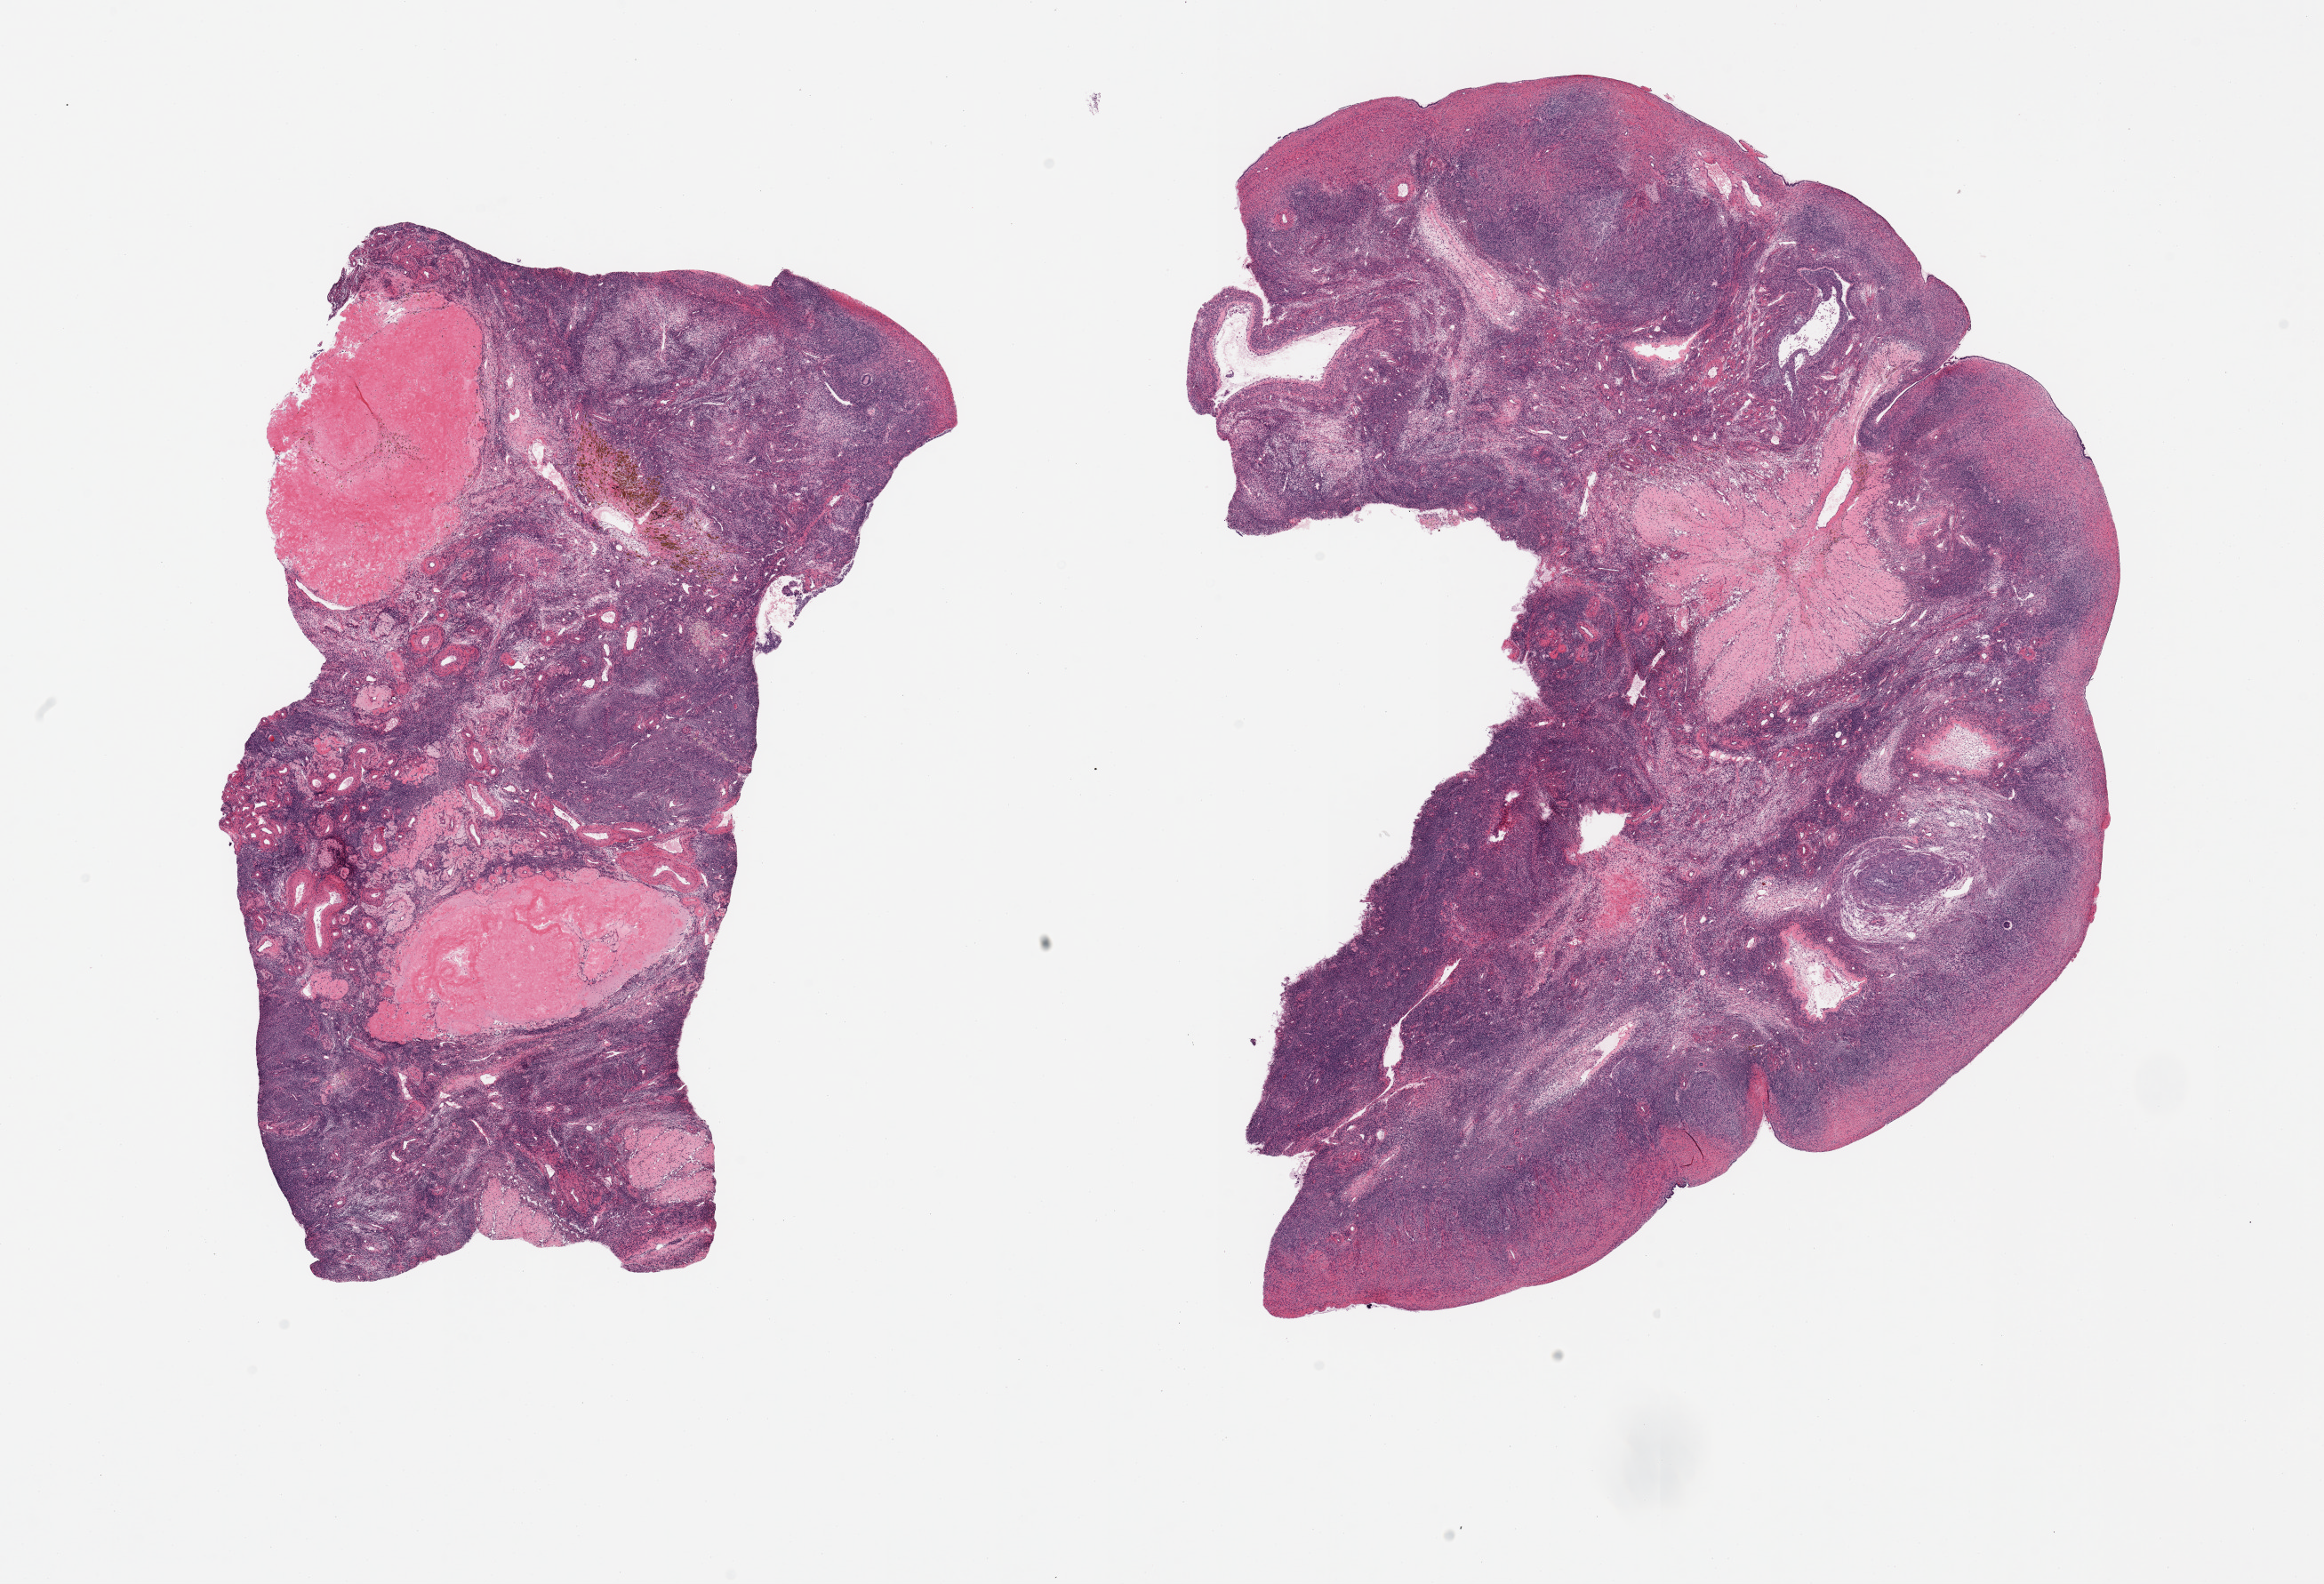
Whole-slide image, H&E stain, brightfield — a low-resolution overview of the entire scanned area, about 20.7 x 14.1 mm (acquisition: 20x scan); PAXgene-fixed paraffin-embedded (PFPE) section; section of ovary (target tissue); donor tissue sample.
- pathologist's review note for this sample: 2 pieces